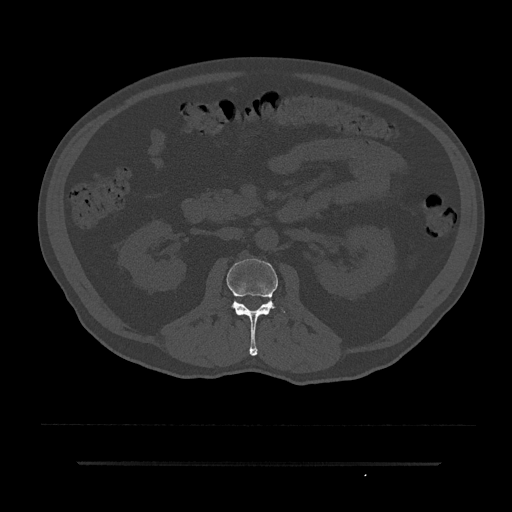
CT including the spine, one axial slice; slice 70 of 797 in the series (ordered by position); bone window (W 1800 / L 400 HU); 512 × 512 image matrix, field of view 464 × 464 mm. Patient: male, 59 years. From the clinical record (not read from this slice): primary cancer: bile ducts; vertebrae with lytic lesions (as recorded): T10.
Outlined on this slice (semi-automatic segmentation, software-assisted and operator-edited):
- L2 vertebra: bounding box [x1, y1, x2, y2] px = [226, 259, 286, 356]